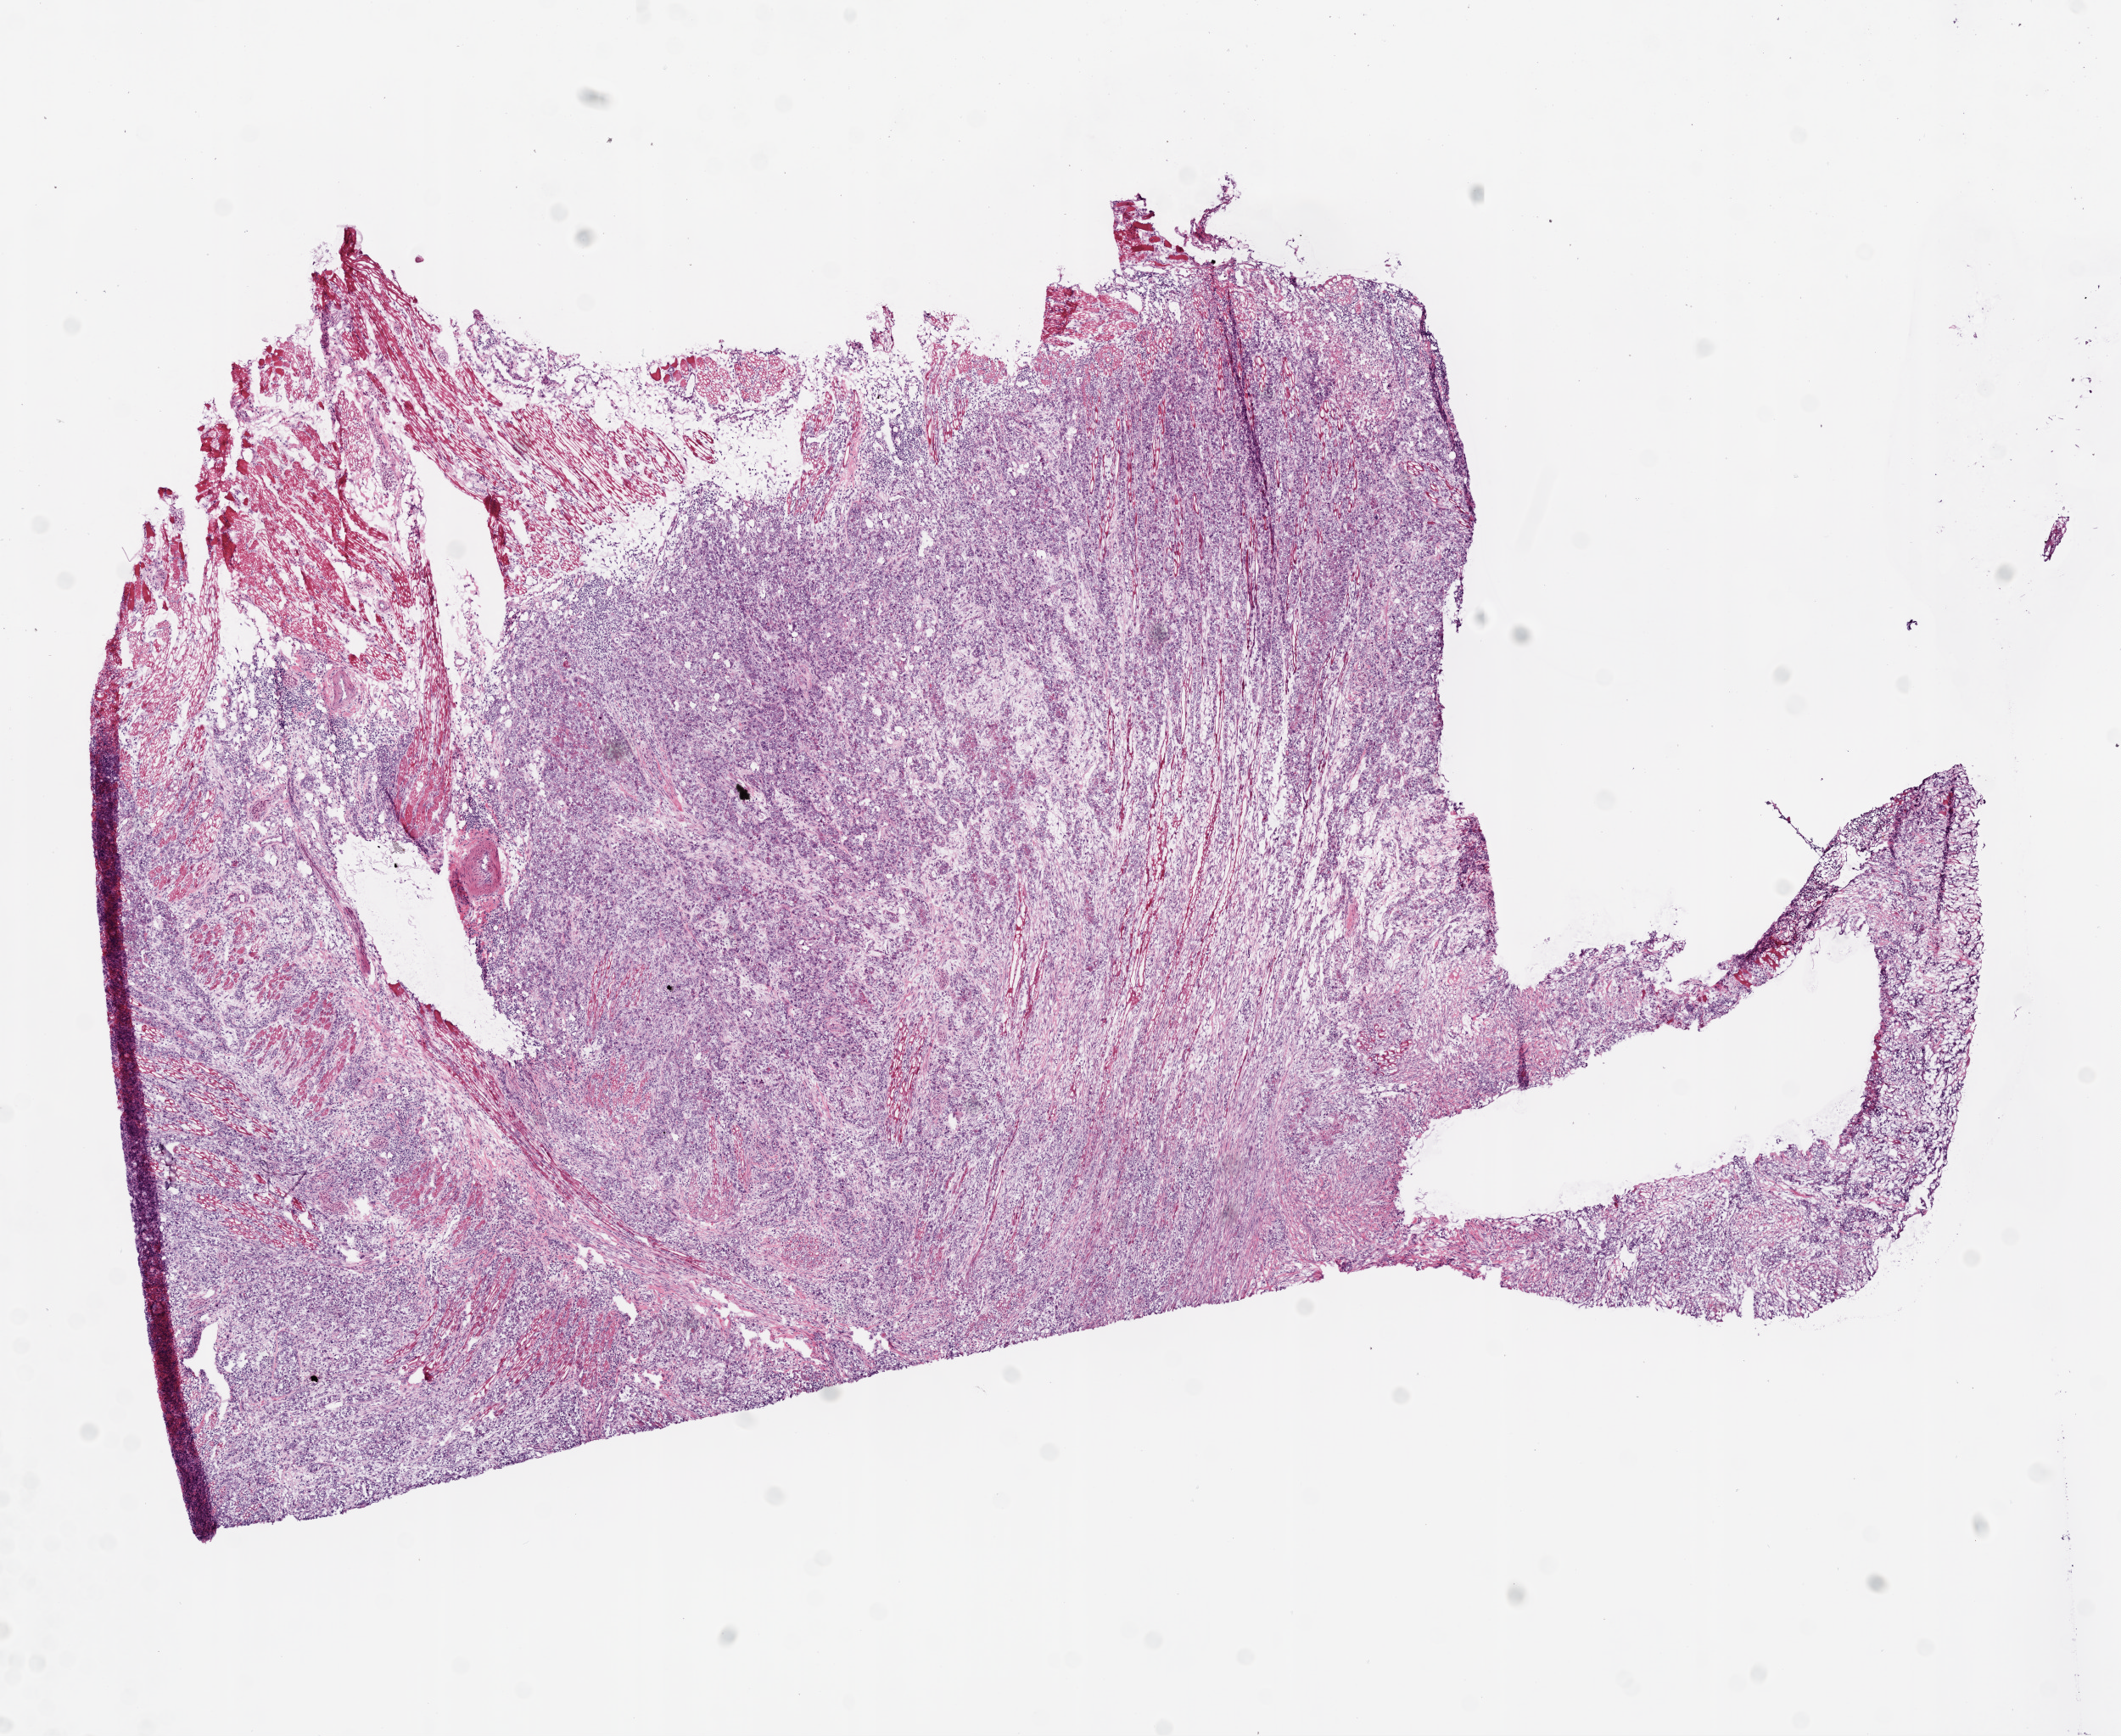
Whole-slide histology image, H&E — low-resolution overview of the scanned area, about 10.0 x 8.2 mm (slide scanned at 20x). Frozen section from the bottom of the tissue portion. Head and neck, primary tumour sample. Female, age 69 years at initial diagnosis.
Diagnosis: Squamous cell carcinoma, NOS (tongue, NOS).